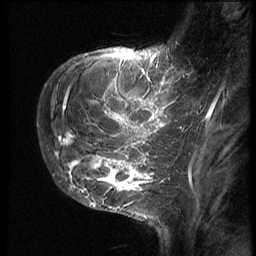
Breast MRI (dynamic contrast-enhanced), one sagittal slice. Slice 14 of 62 in the series (ordered by position). 3 images stored at this slice position (order not interpretable as contrast timing). 1.5 T. TE 4.2 ms, TR 9 ms. 2.5 mm slice thickness. 256 × 256 image matrix. Patient: female, 28 years. Case-level facts recorded for this patient, not image findings: setting: breast cancer imaged before/during neoadjuvant chemotherapy.
Annotated regions visible in this slice (semi-automatic segmentation, software-assisted and operator-edited):
- analysis volume of interest (the breast-tissue region the enhancement analysis was run in; not a lesion): box from (x=42, y=68) to (x=192, y=202) px
- tumour enhancement mask (voxels above the 140 % enhancement threshold inside the analysis volume of interest): (x=54, y=71)–(x=191, y=192)